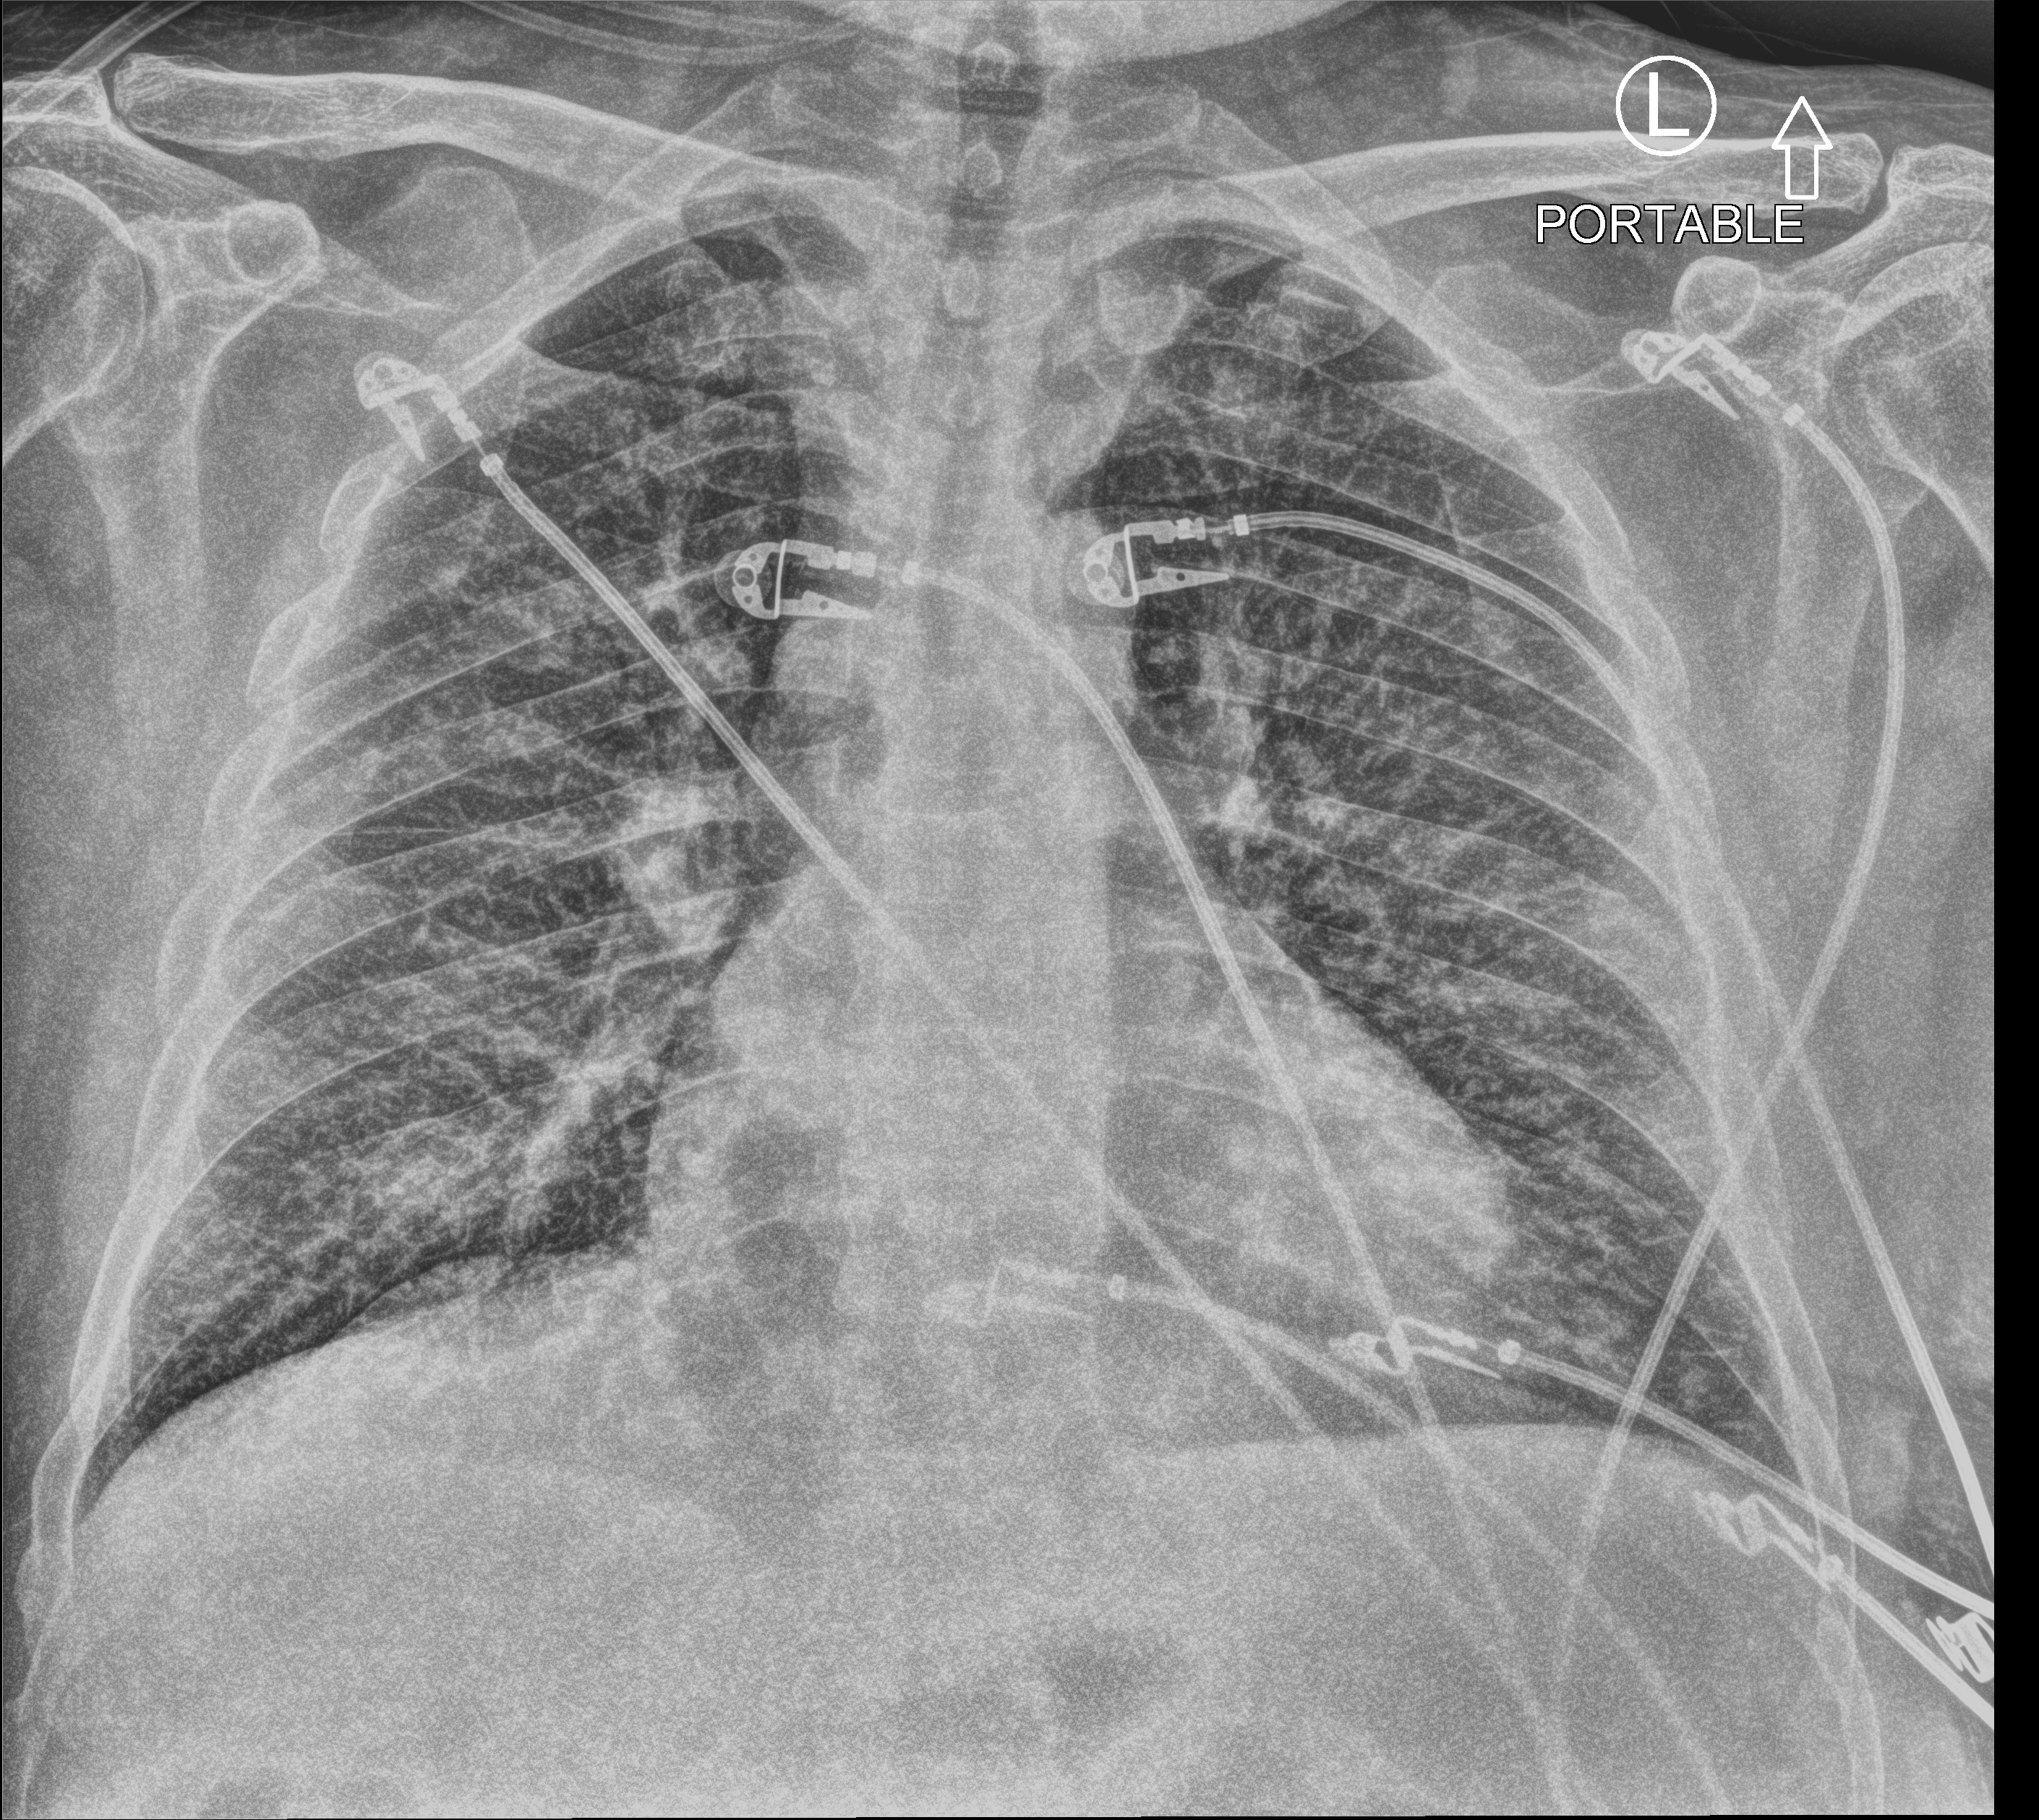
Chest X-ray (portable), anteroposterior (AP) projection. Patient hospitalised with COVID-19; male, aged 60–74 years.
Admission-level facts for this patient (not findings on this image; timing relative to this image not recorded):
- mechanically ventilated during this hospital stay: no